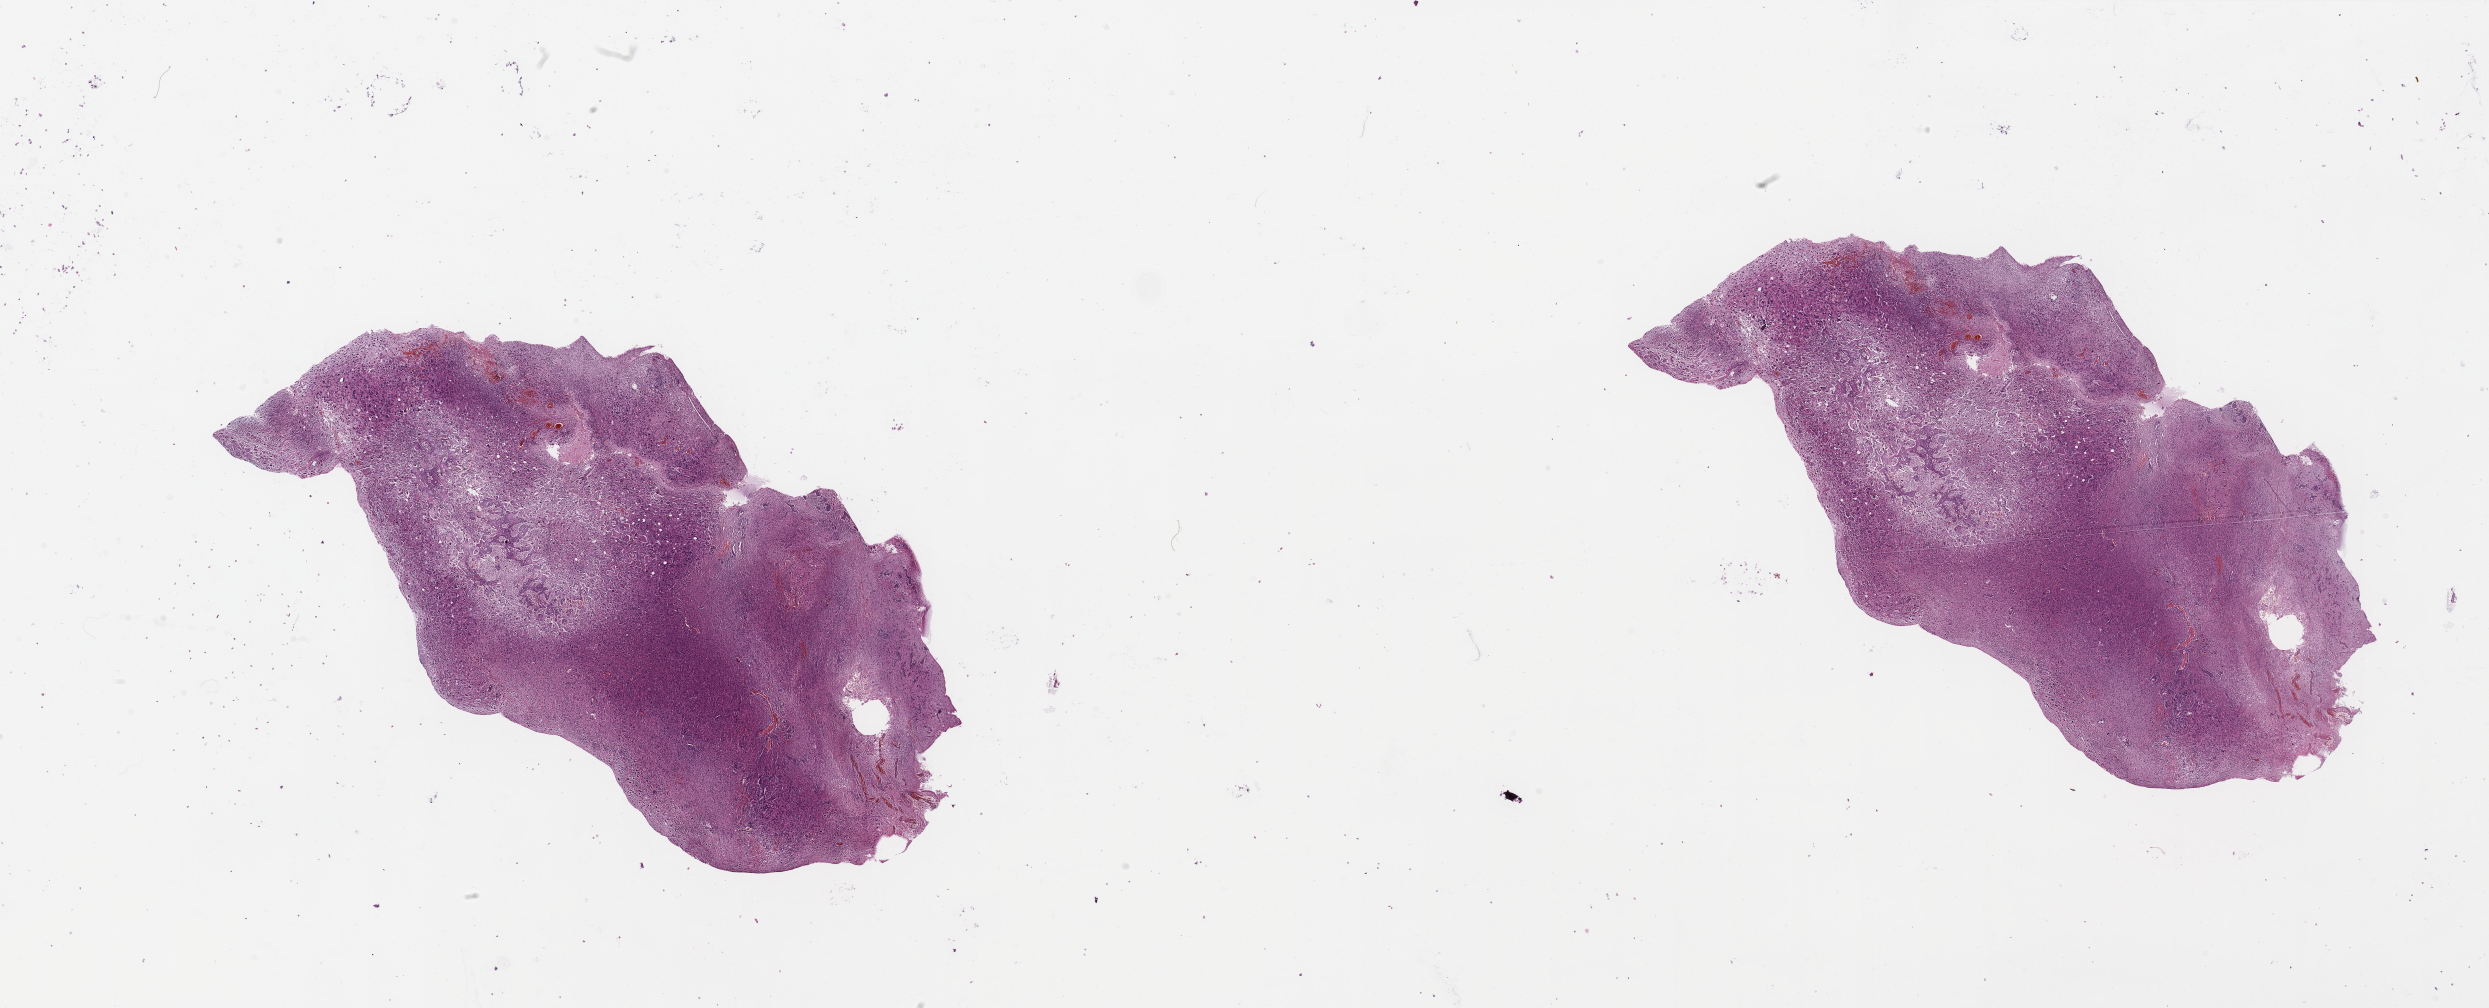
H&E whole-slide image, a low-resolution overview of the entire scanned area, about 39.4 x 15.9 mm, brain, tumour tissue. Male, 77 y/o.
- histologic diagnosis: Glioblastoma
- primary tumour site (as recorded): frontal lobe